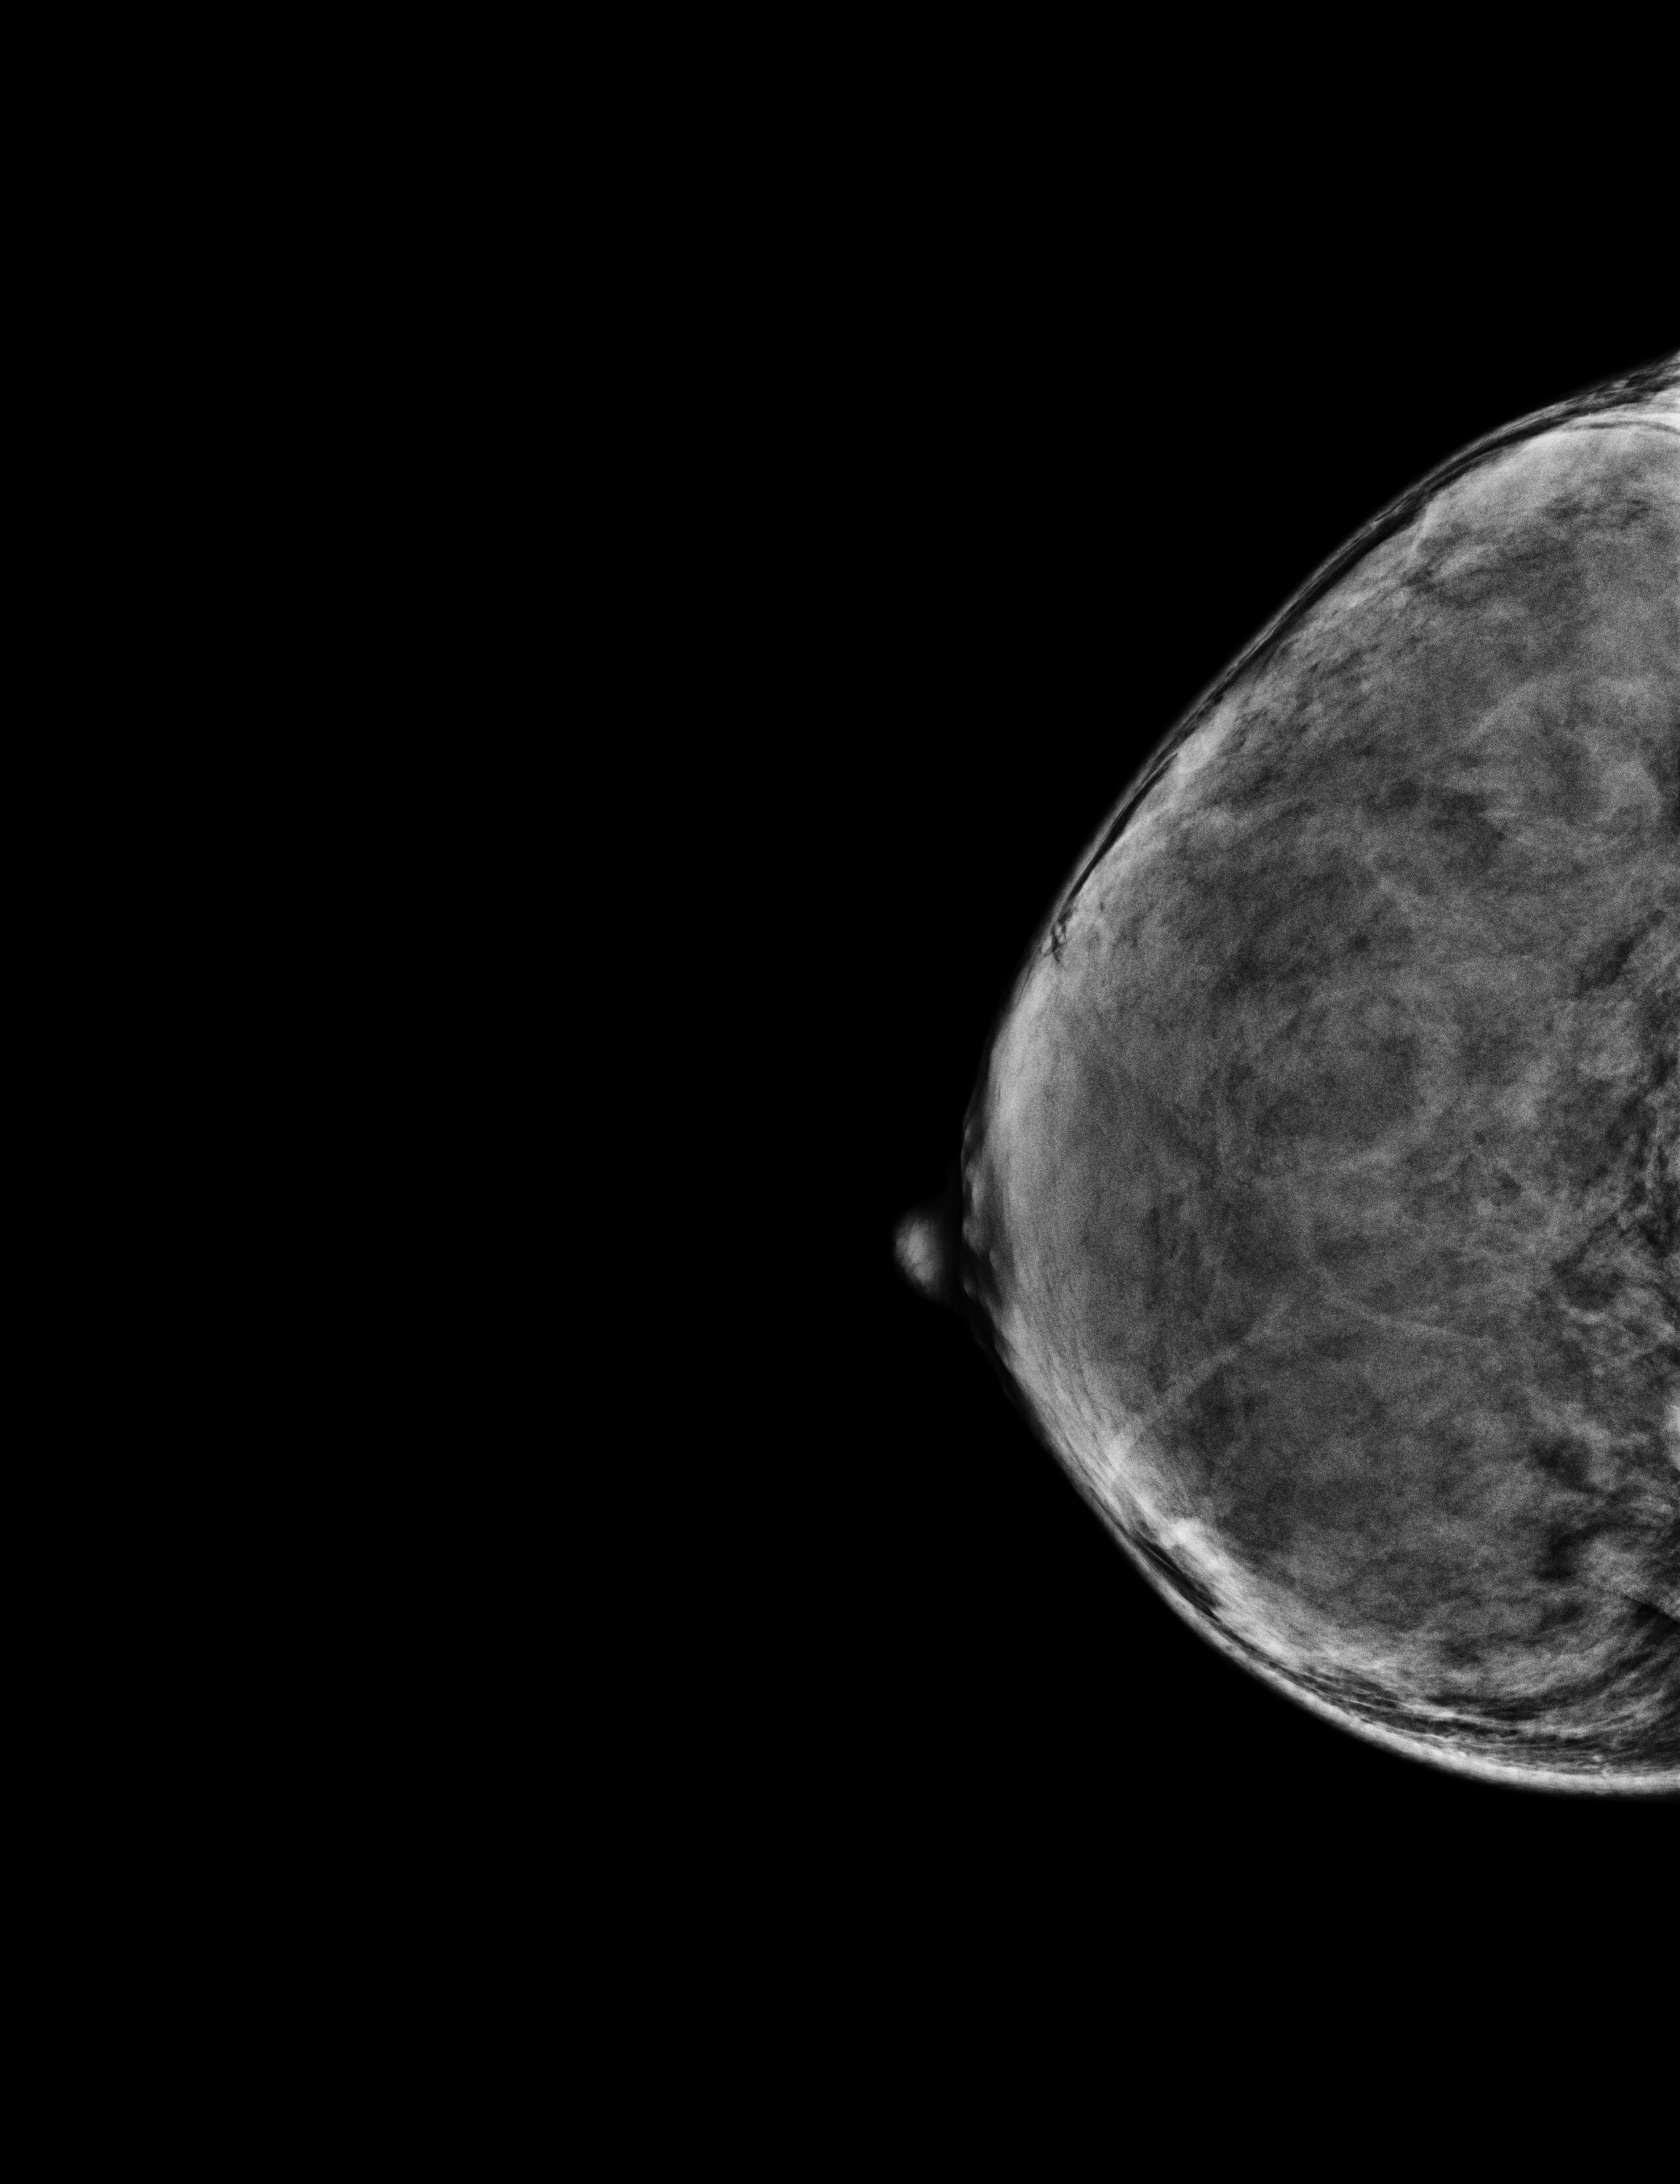
Digital mammogram (FFDM); right breast; cranio-caudal projection; annual screening mammography examination; compressed breast thickness 36 mm. Patient: female, 54 years.
BI-RADS breast density category at the screening exam (both breasts, scale 1–4): 4. Final BI-RADS category for the screening round (tomosynthesis exam, both breasts): category 1. Recall: no recall after this screen.